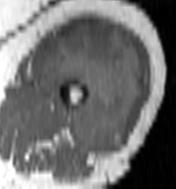
MRI of an extremity soft-tissue mass, one axial slice; position 65 of 100 along the scan axis; MR volume resampled by the dataset authors to the PET/CT grid (not the native acquisition matrix); 3.27 mm slice thickness; 176 × 189 image matrix, field of view 172 × 185 mm. Female patient. From the clinical record (not read from this slice): histological type: undifferentiated – high grade; grade: high; site of the primary tumour: left thigh.
Outlined on this slice (expert contour drawn on MRI and transferred to this co-registered scan by the dataset authors):
- gross tumour volume including surrounding oedema: bounding box [x1, y1, x2, y2] px = [46, 23, 143, 154]
- gross tumour volume (mass): [46, 23, 141, 154]